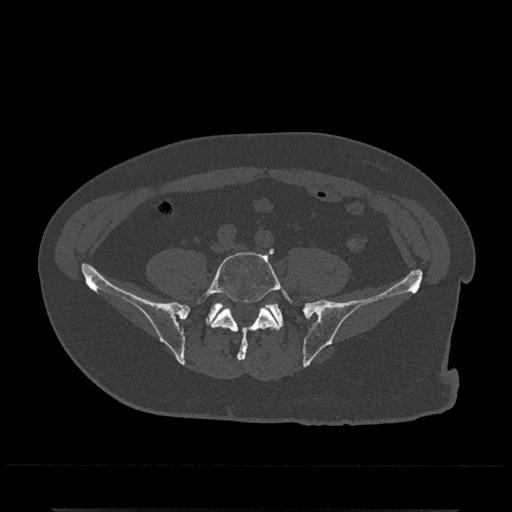
CT including the spine, one axial slice; slice 76 of 797 in the series (ordered by position); reconstruction kernel Br40s/3; 120 kVp; bone window (W 1800 / L 400 HU); 0.5 mm slice thickness; 512 × 512 image matrix. Male patient, age 67 years. From the clinical record (not read from this slice): primary cancer: prostate.
Outlined on this slice (semi-automatic segmentation, software-assisted and operator-edited):
- L5 vertebra: bounding box (x1, y1, x2, y2) in pixels: (197, 249, 293, 361)